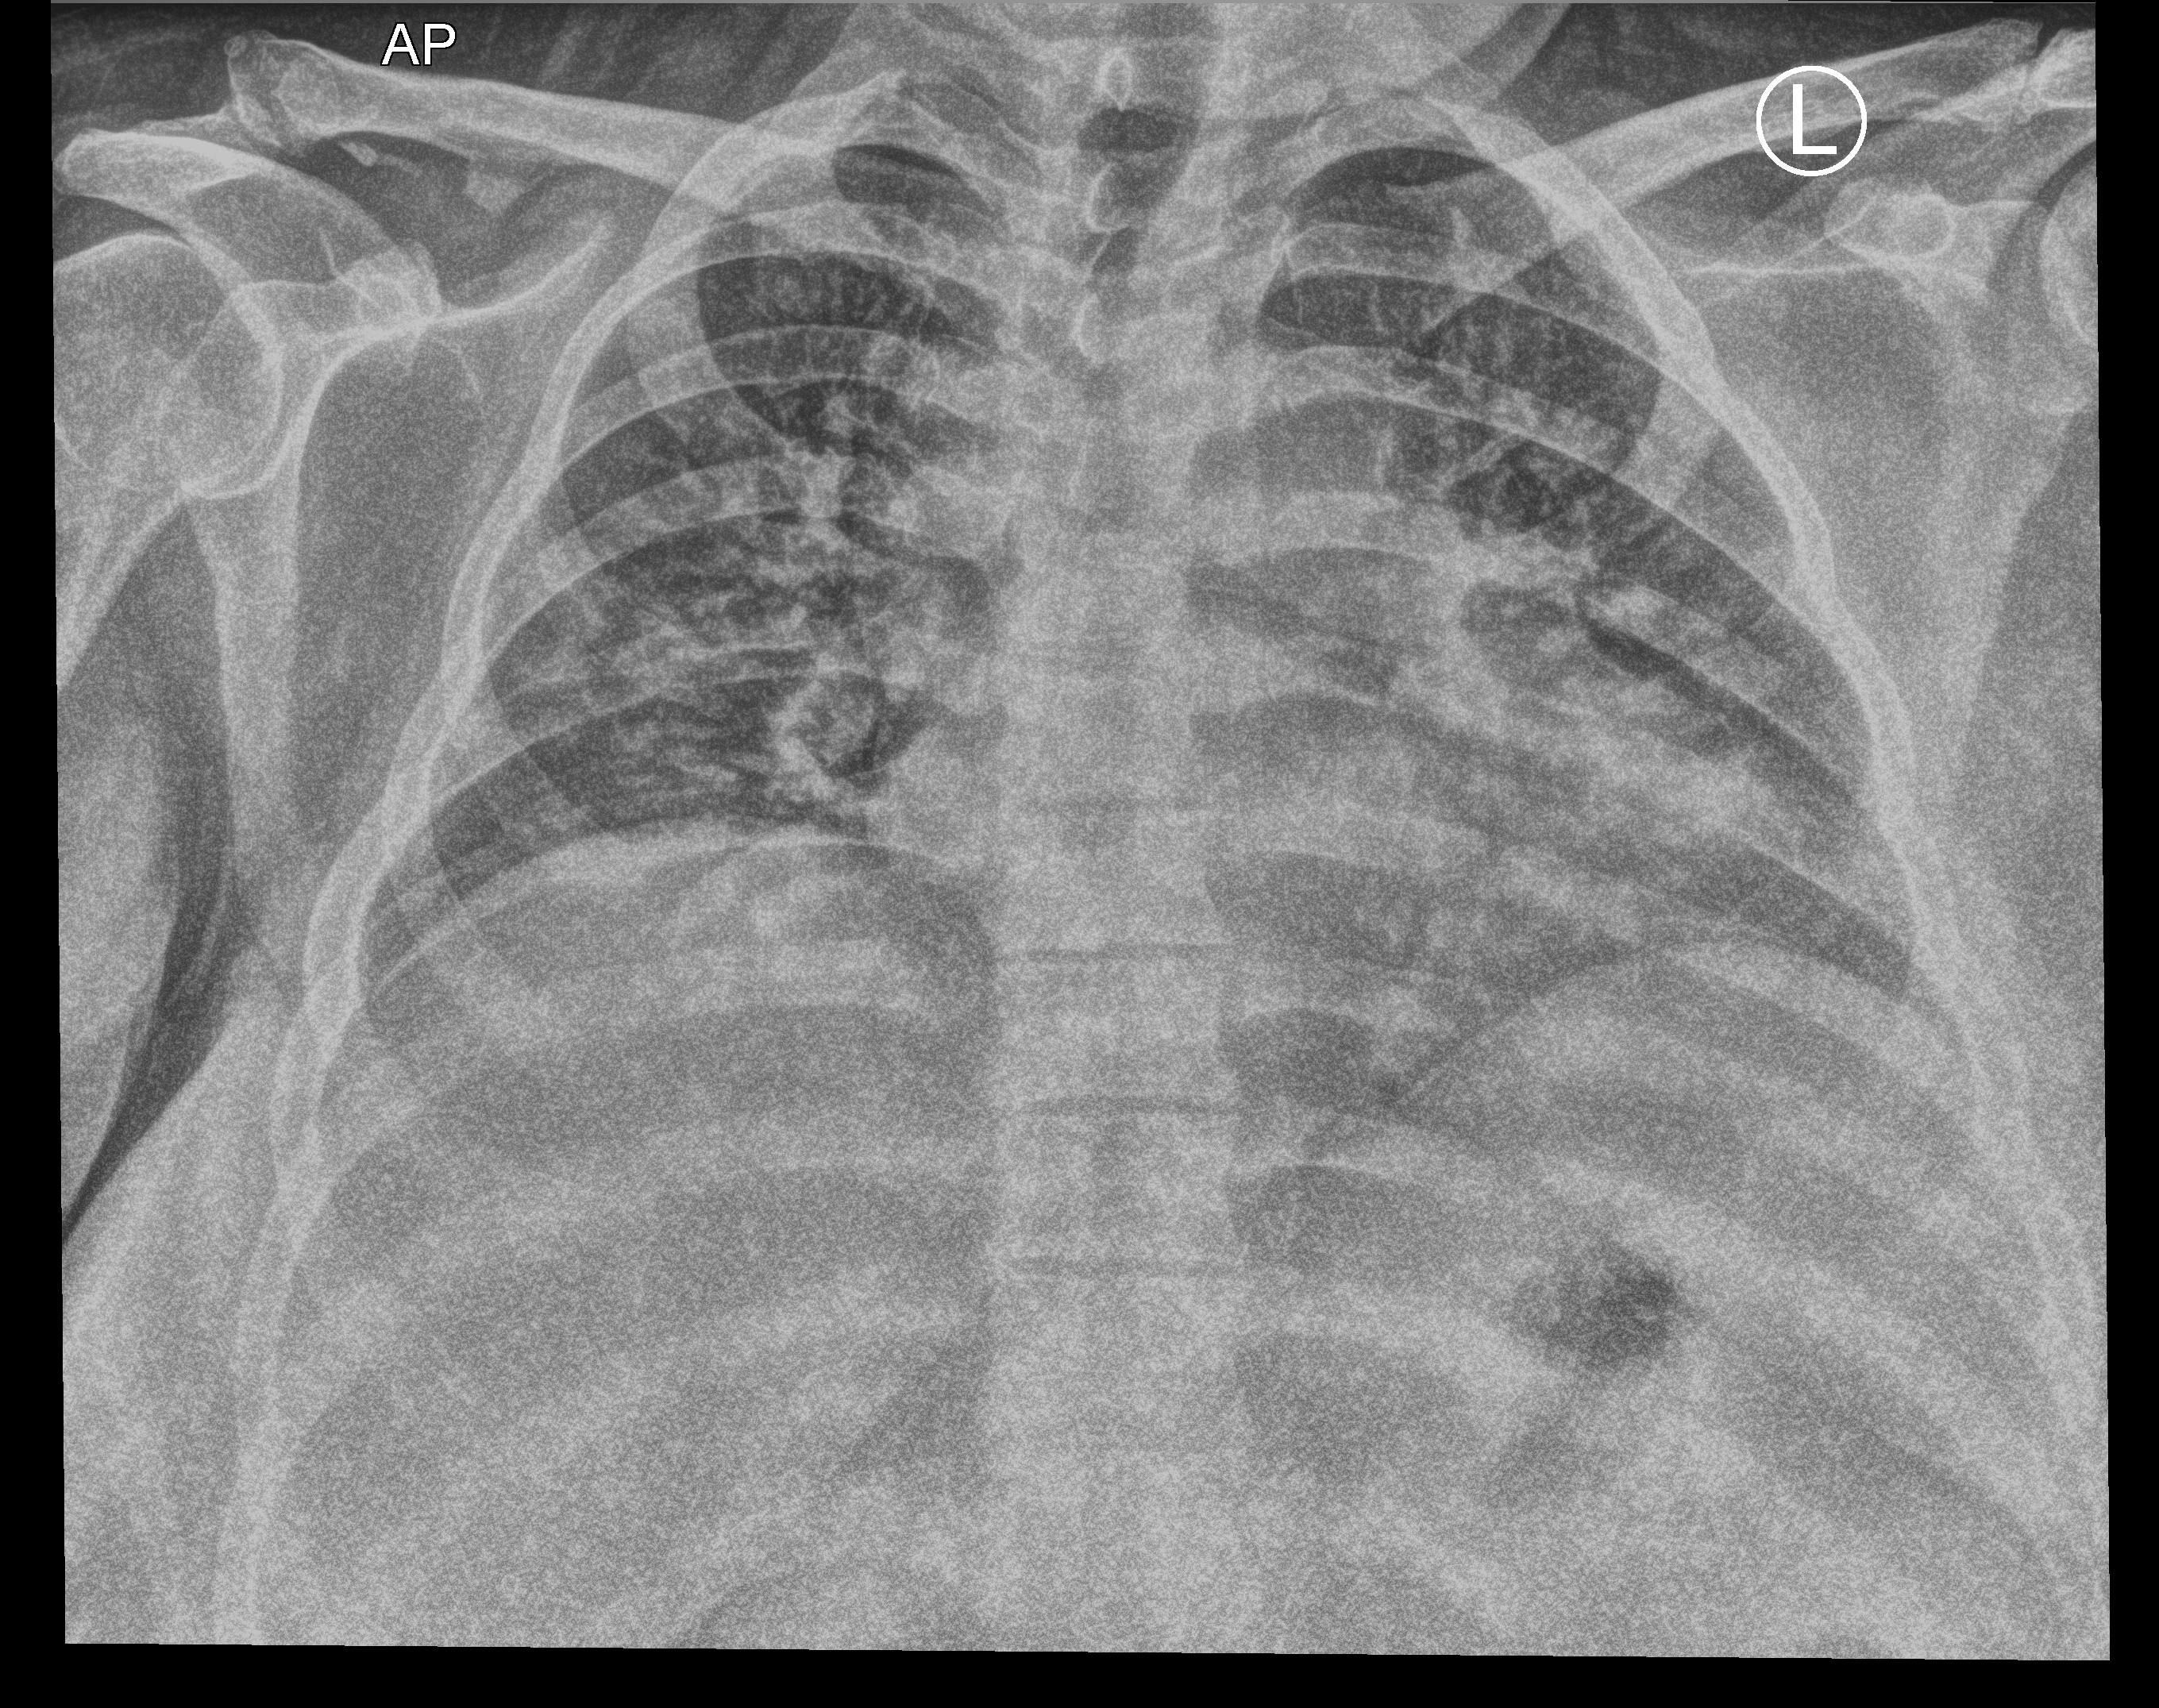
Chest X-ray (portable), anteroposterior (AP) projection. Patient hospitalised with COVID-19; female, aged 18–59 years.
From the hospital-stay record, not from the radiograph (when in the stay this image was taken is not recorded): length of hospital stay: 25 days; smoking status (admission record): never.